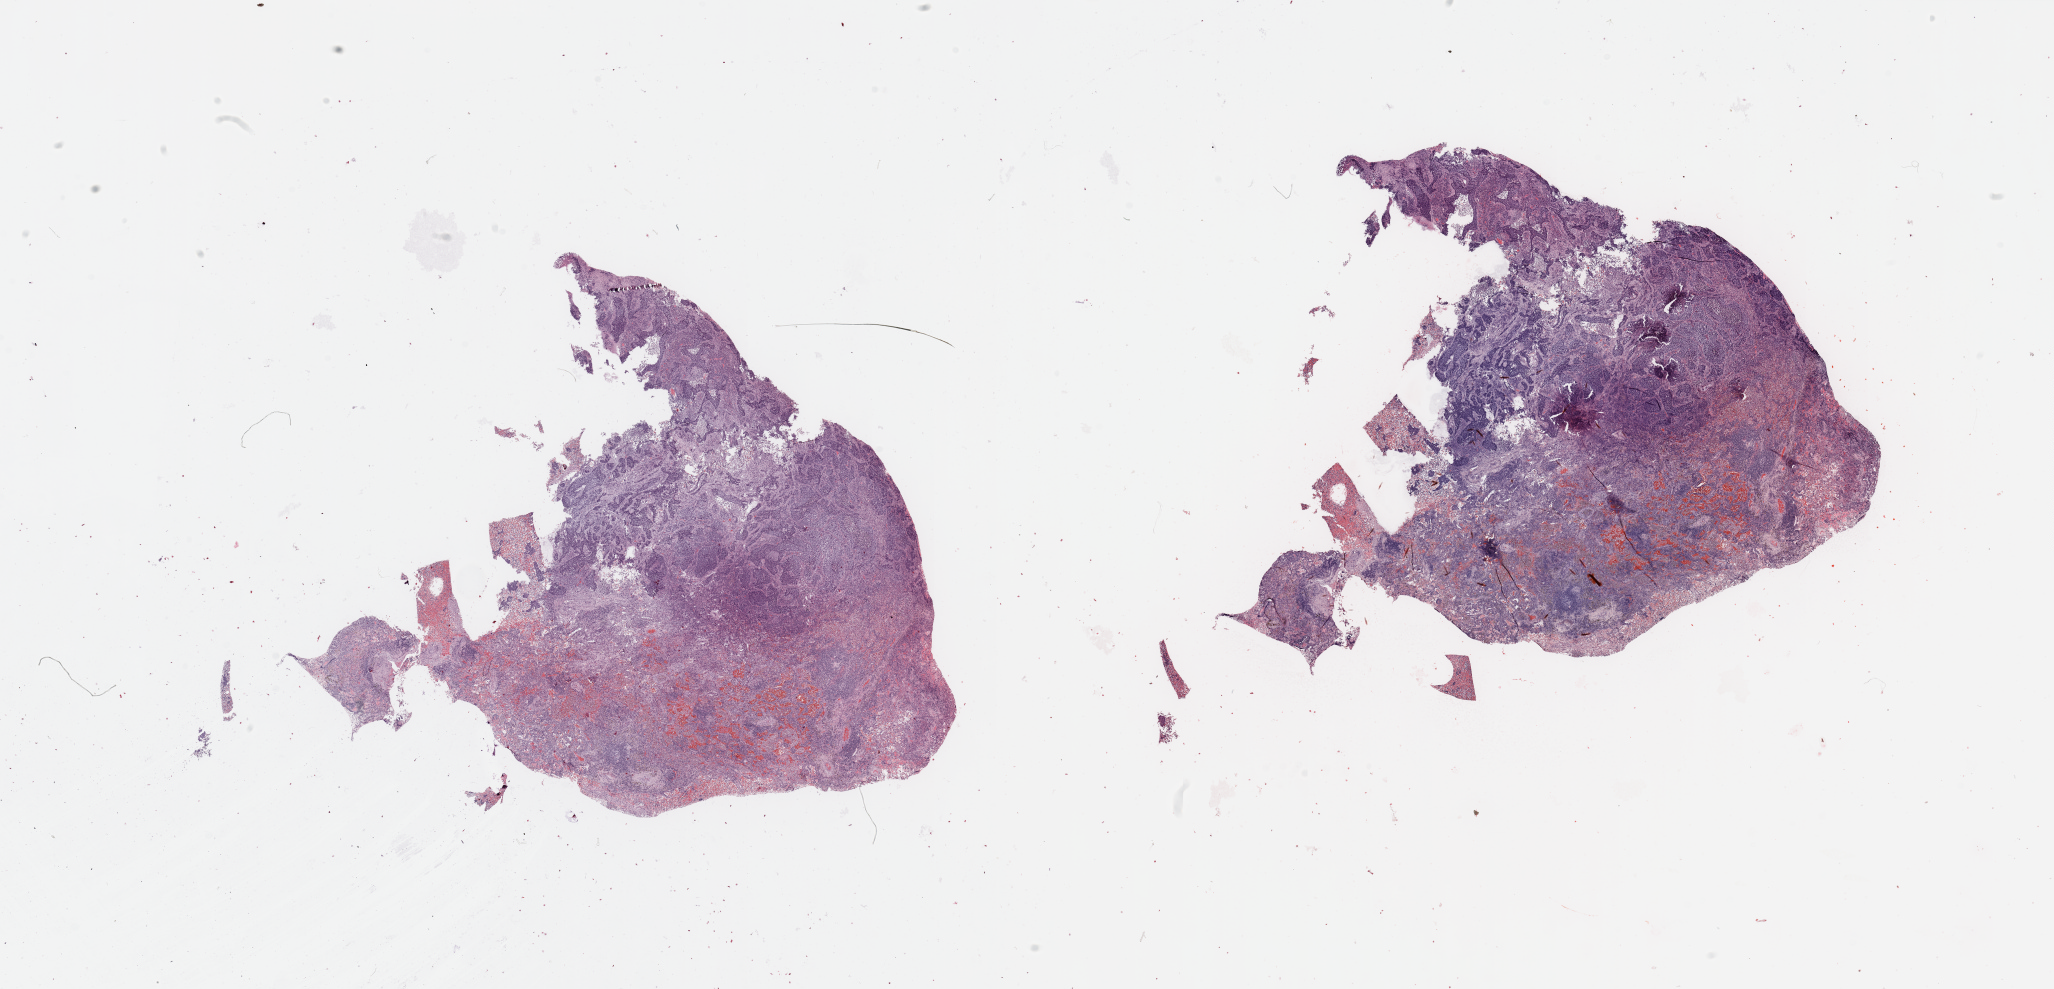
Digitized Hematoxylin and eosin (H&E) stained tissue section (whole slide) — low-resolution overview of the scanned area, about 32.5 x 15.6 mm, lung, tumour tissue. 73-year-old male patient.
Diagnosis: Squamous cell carcinoma, NOS.